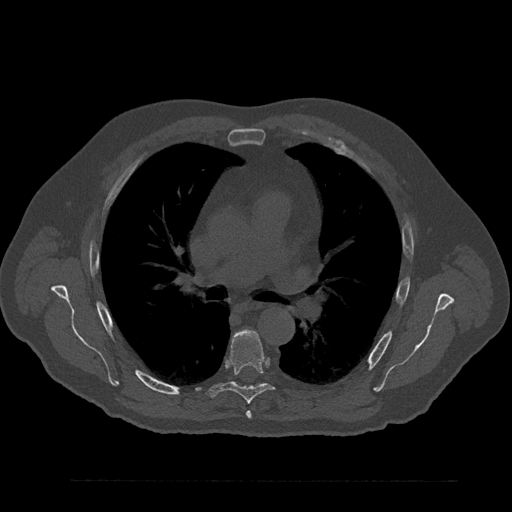
CT including the spine, one axial slice. Slice 558 of 797 in the series (ordered by position). Reconstruction kernel Br40s/3. 120 kVp. Bone window (W 1800 / L 400 HU). 0.5 mm slice thickness. 512 × 512 image matrix, field of view 430 × 430 mm. Patient: male, 61 years. Case-level facts recorded for this patient, not image findings: primary cancer: prostate.
Structures marked on this image (semi-automatic segmentation, software-assisted and operator-edited):
- T5 vertebra: bounding box [x1, y1, x2, y2] px = [246, 411, 252, 419]
- T6 vertebra: [207, 330, 275, 404]